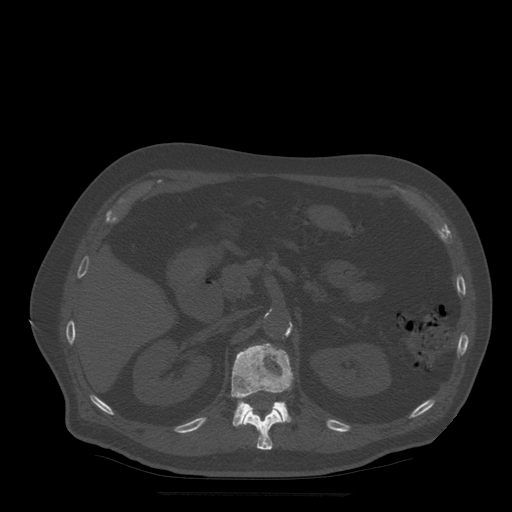
CT including the spine, one axial slice; slice 206 of 522 in the series (ordered by position); bone window (W 1800 / L 400 HU); 1.25 mm slice thickness; 512 × 512 image matrix. Patient age 72 years. Case-level facts recorded for this patient, not image findings: primary cancer: prostate.
Outlined on this slice (semi-automatically segmented with operator editing):
- L1 vertebra: box from (x=232, y=344) to (x=293, y=427) px
- T12 vertebra: (x=244, y=408)–(x=283, y=450)